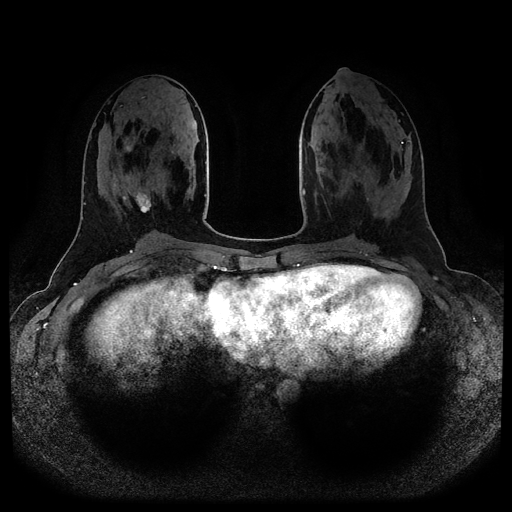
Breast MRI (dynamic contrast-enhanced, multi-phase), one axial slice; position 41 of 116 along the scan axis; dynamic contrast-enhanced series, time point 2 of 5 at this slice position (early post-contrast); 1.5 T; TE 2.6 ms, TR 5.2 ms; 2 mm slice thickness; 512 × 512 image matrix, field of view 380 × 380 mm. Patient: female, 25 years.
Structures marked on this image (semi-automatically segmented with operator editing):
- breast lesion (labelled benign in the annotation): box from (x=135, y=192) to (x=152, y=213) px